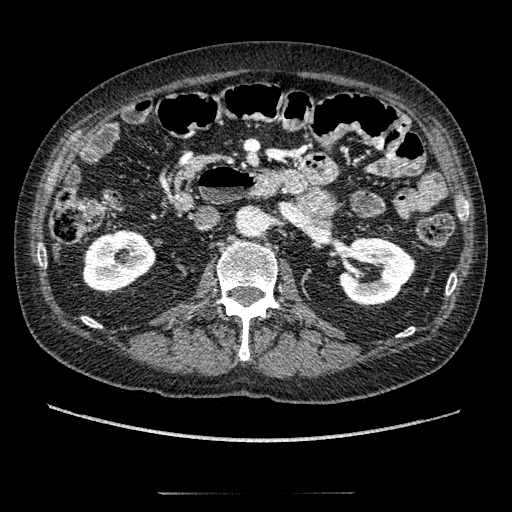
Contrast-enhanced abdominal CT, one axial slice. Slice 82 of 274 in the series (ordered by position). Reconstruction kernel STANDARD. 120 kVp. Intravenous contrast given. Soft-tissue window (W 400 / L 40 HU). 1.25 mm slice thickness. 512 × 512 image matrix, field of view 381 × 381 mm. Male patient, age 69 years. From the clinical record (not read from this slice): diagnosis: adrenocortical carcinoma; tumour side: left adrenal; tumour size at pathology: 6.1 cm; Ki-67 index: 10 %; stage (as recorded): 3.
Outlined on this slice (semi-automatic segmentation, software-assisted and operator-edited):
- mass: bounding box [x1, y1, x2, y2] px = [302, 191, 334, 216]